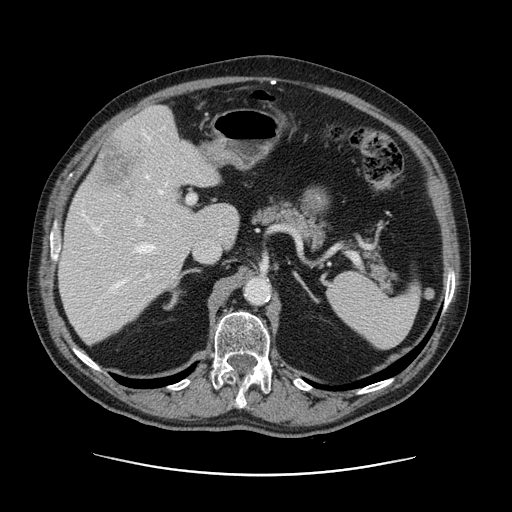
Contrast-enhanced abdominal CT, one axial slice. 120 kVp. Intravenous contrast given. Soft-tissue window (W 400 / L 40 HU). 2.5 mm slice thickness. 512 × 512 image matrix, field of view 395 × 395 mm. Male patient, age 72 years. From the clinical record (not read from this slice): diagnosis: colorectal cancer liver metastases, imaged before liver resection; multiple liver metastases: yes; largest metastasis: 5.4 cm.
Outlined on this slice (expert manual segmentation):
- hepatic veins: bounding box <97,129,168,303> (left, top, right, bottom; pixels)
- liver: <59,106,239,344>
- planned liver remnant (the part of the liver to remain after resection): <59,147,239,344>
- portal vein (with intrahepatic branches): <83,195,196,303>
- liver metastasis: <99,141,140,194>